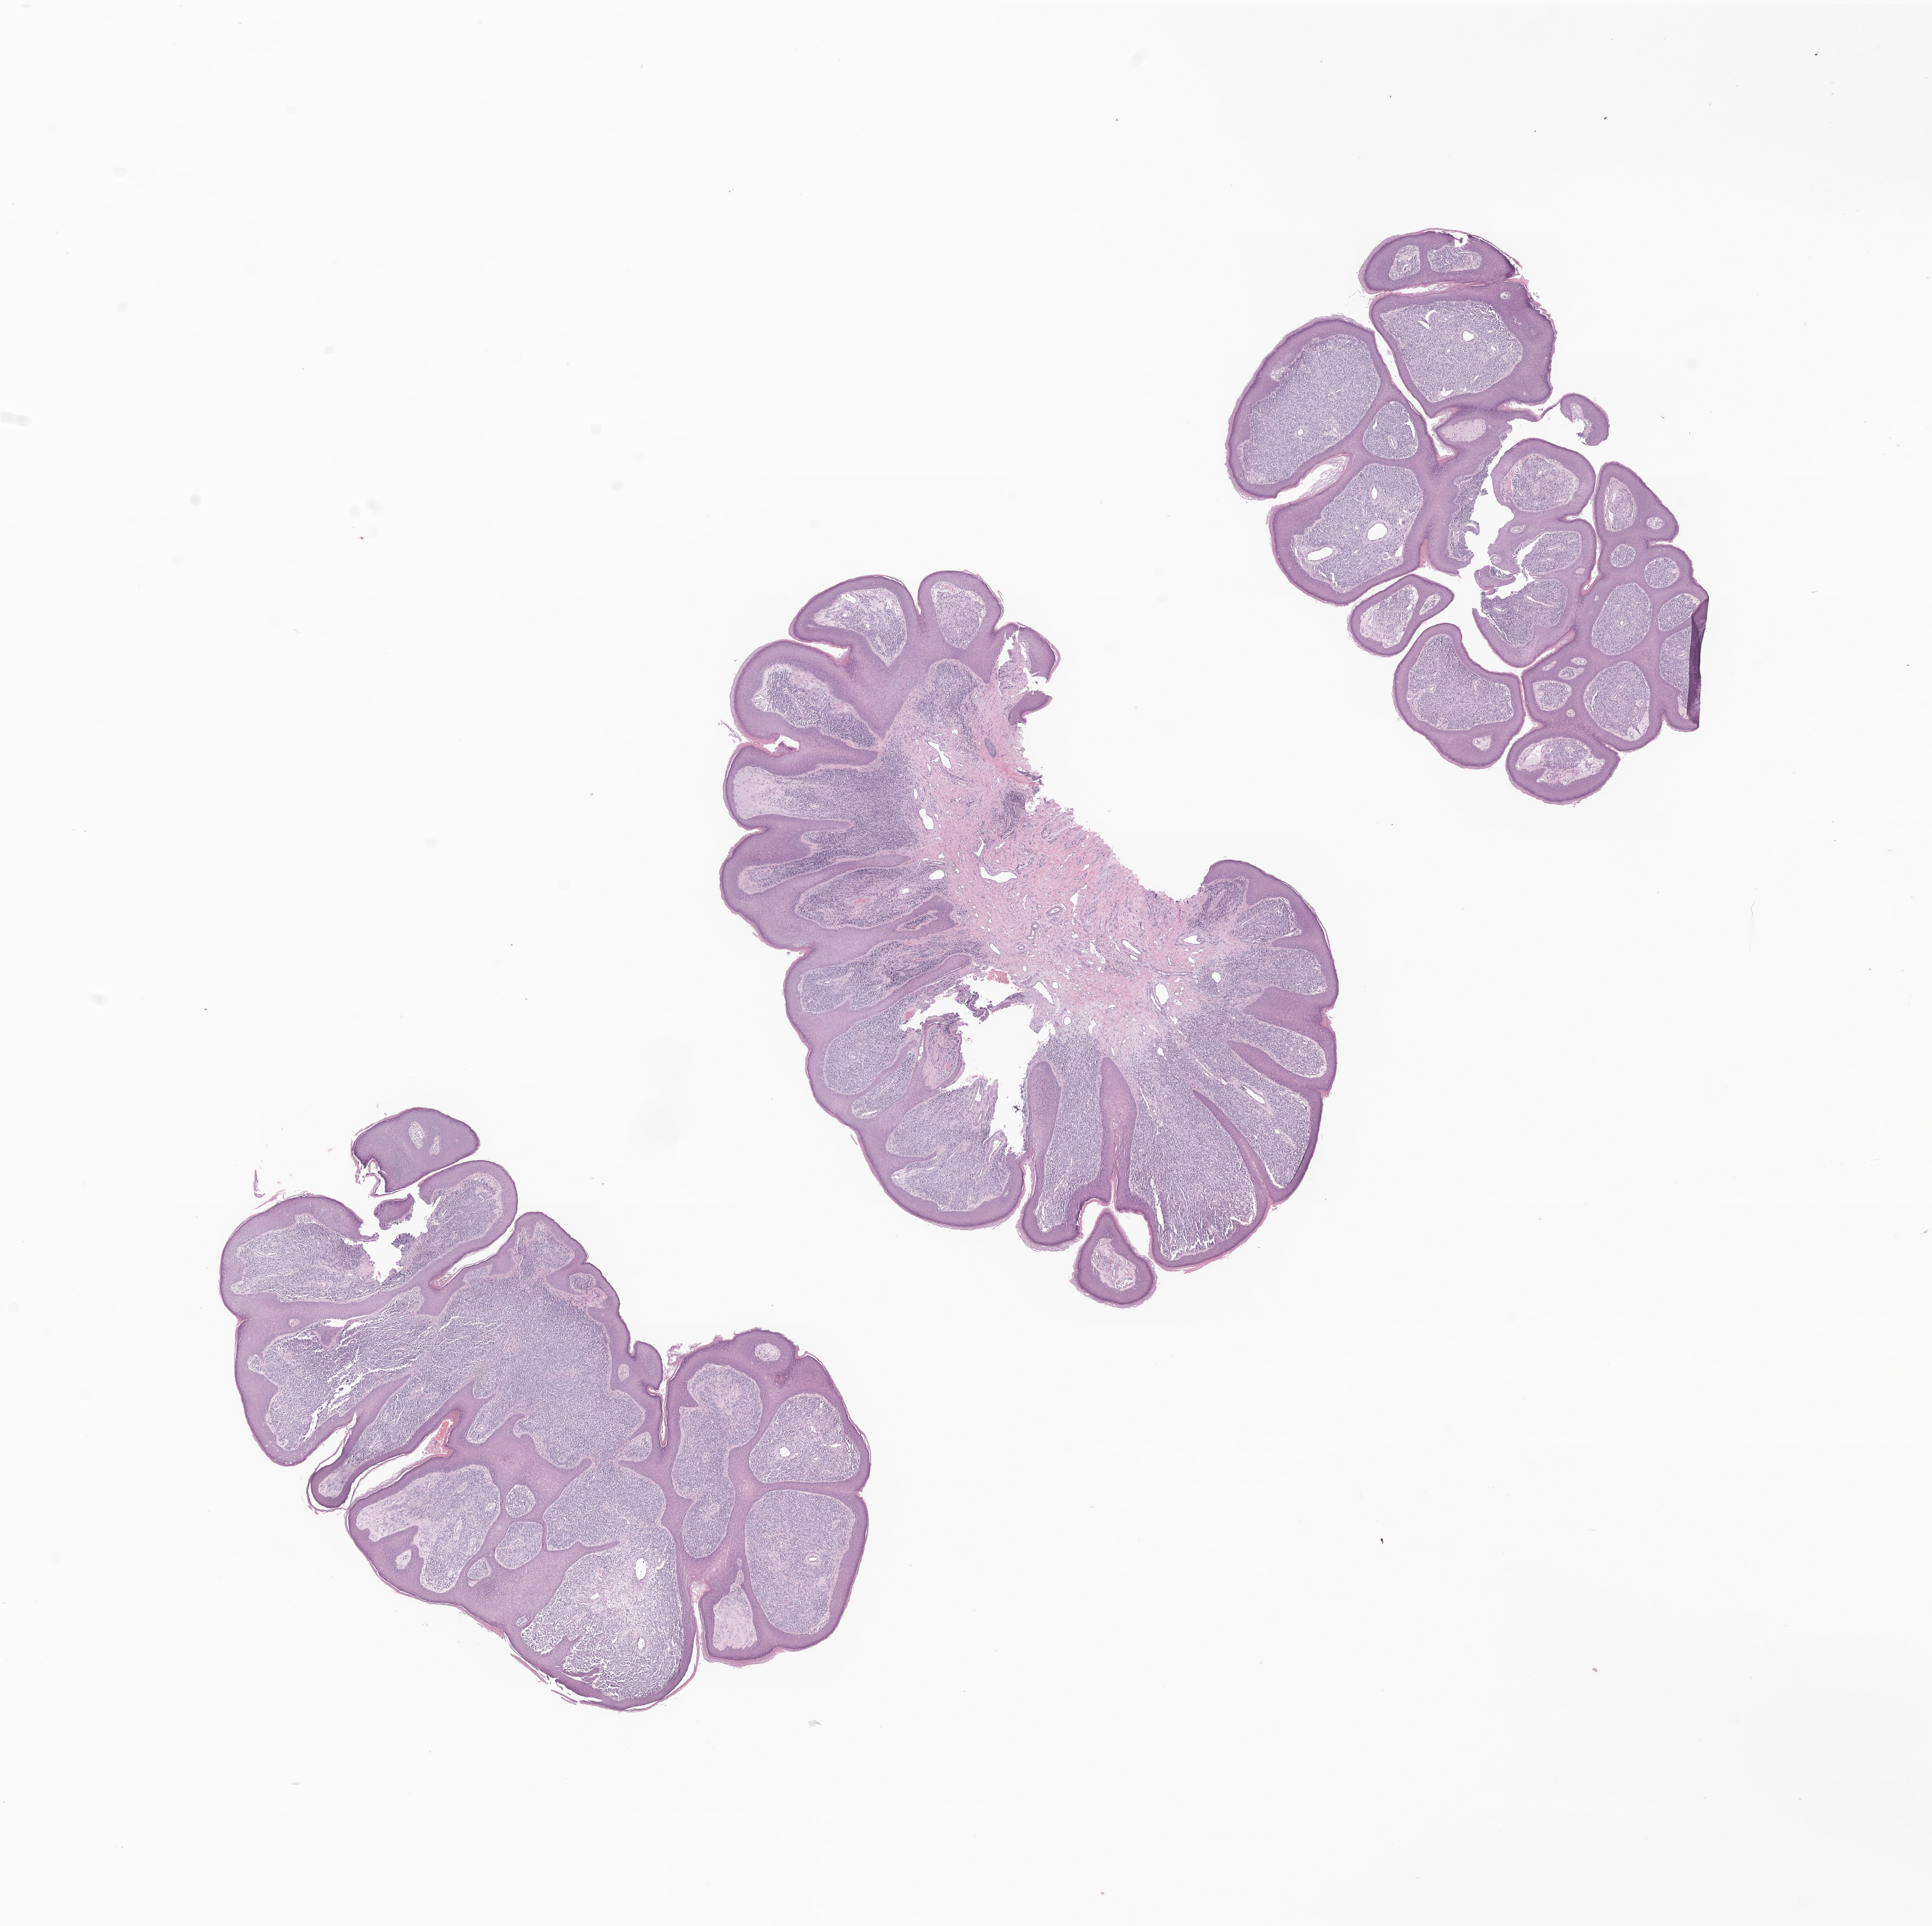
Whole-slide image, haematoxylin and eosin stain of tumor tissue from the commissure of lip — shown as a low-resolution overview of the whole scanned area (about 17.0 x 17.0 mm), FFPE section. Male patient, age 764 days (about 2.1 years).
- diagnosis: Embryonal rhabdomyosarcoma, NOS